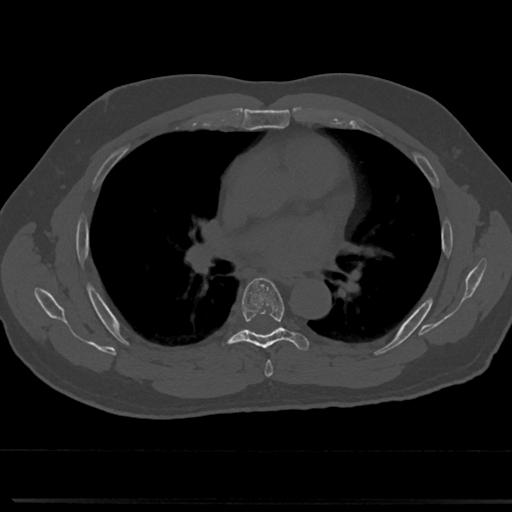
CT including the spine, one axial slice. Slice 456 of 817 in the series (ordered by position). Reconstruction kernel Br40s/3. 120 kVp. Bone window (W 1800 / L 400 HU). 0.5 mm slice thickness. 512 × 512 image matrix. Patient: male, 61 years. From the clinical record (not read from this slice): primary cancer: prostate.
Annotated regions visible in this slice (semi-automatically segmented with operator editing):
- T5 vertebra: bounding box [x1, y1, x2, y2] px = [259, 343, 271, 372]
- T6 vertebra: [217, 276, 309, 356]